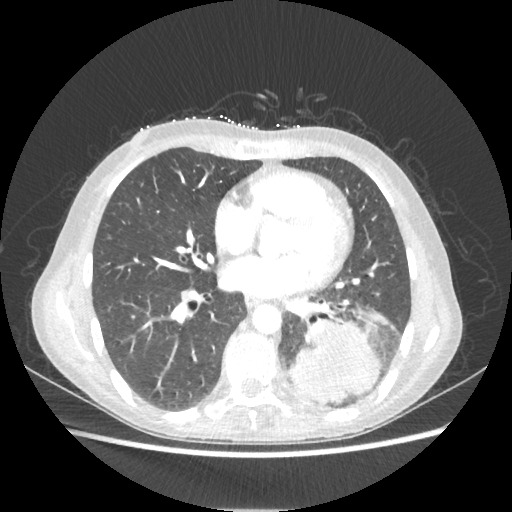
Chest CT, one axial slice; position 98 of 221 along the scan axis; reconstruction kernel STANDARD; 80 kVp; lung window (W 1500 / L -600 HU); 1.25 mm slice thickness; 512 × 512 image matrix, field of view 360 × 360 mm. Female patient, age 53 years. Case-level facts recorded for this patient, not image findings: clinical TNM (as recorded): T3 N0 M0.
Annotated regions visible in this slice (rectangle marked by the reading radiologist):
- lung tumour (recorded histology: adenocarcinoma): bounding box (x1, y1, x2, y2) in pixels: (286, 321, 380, 403)